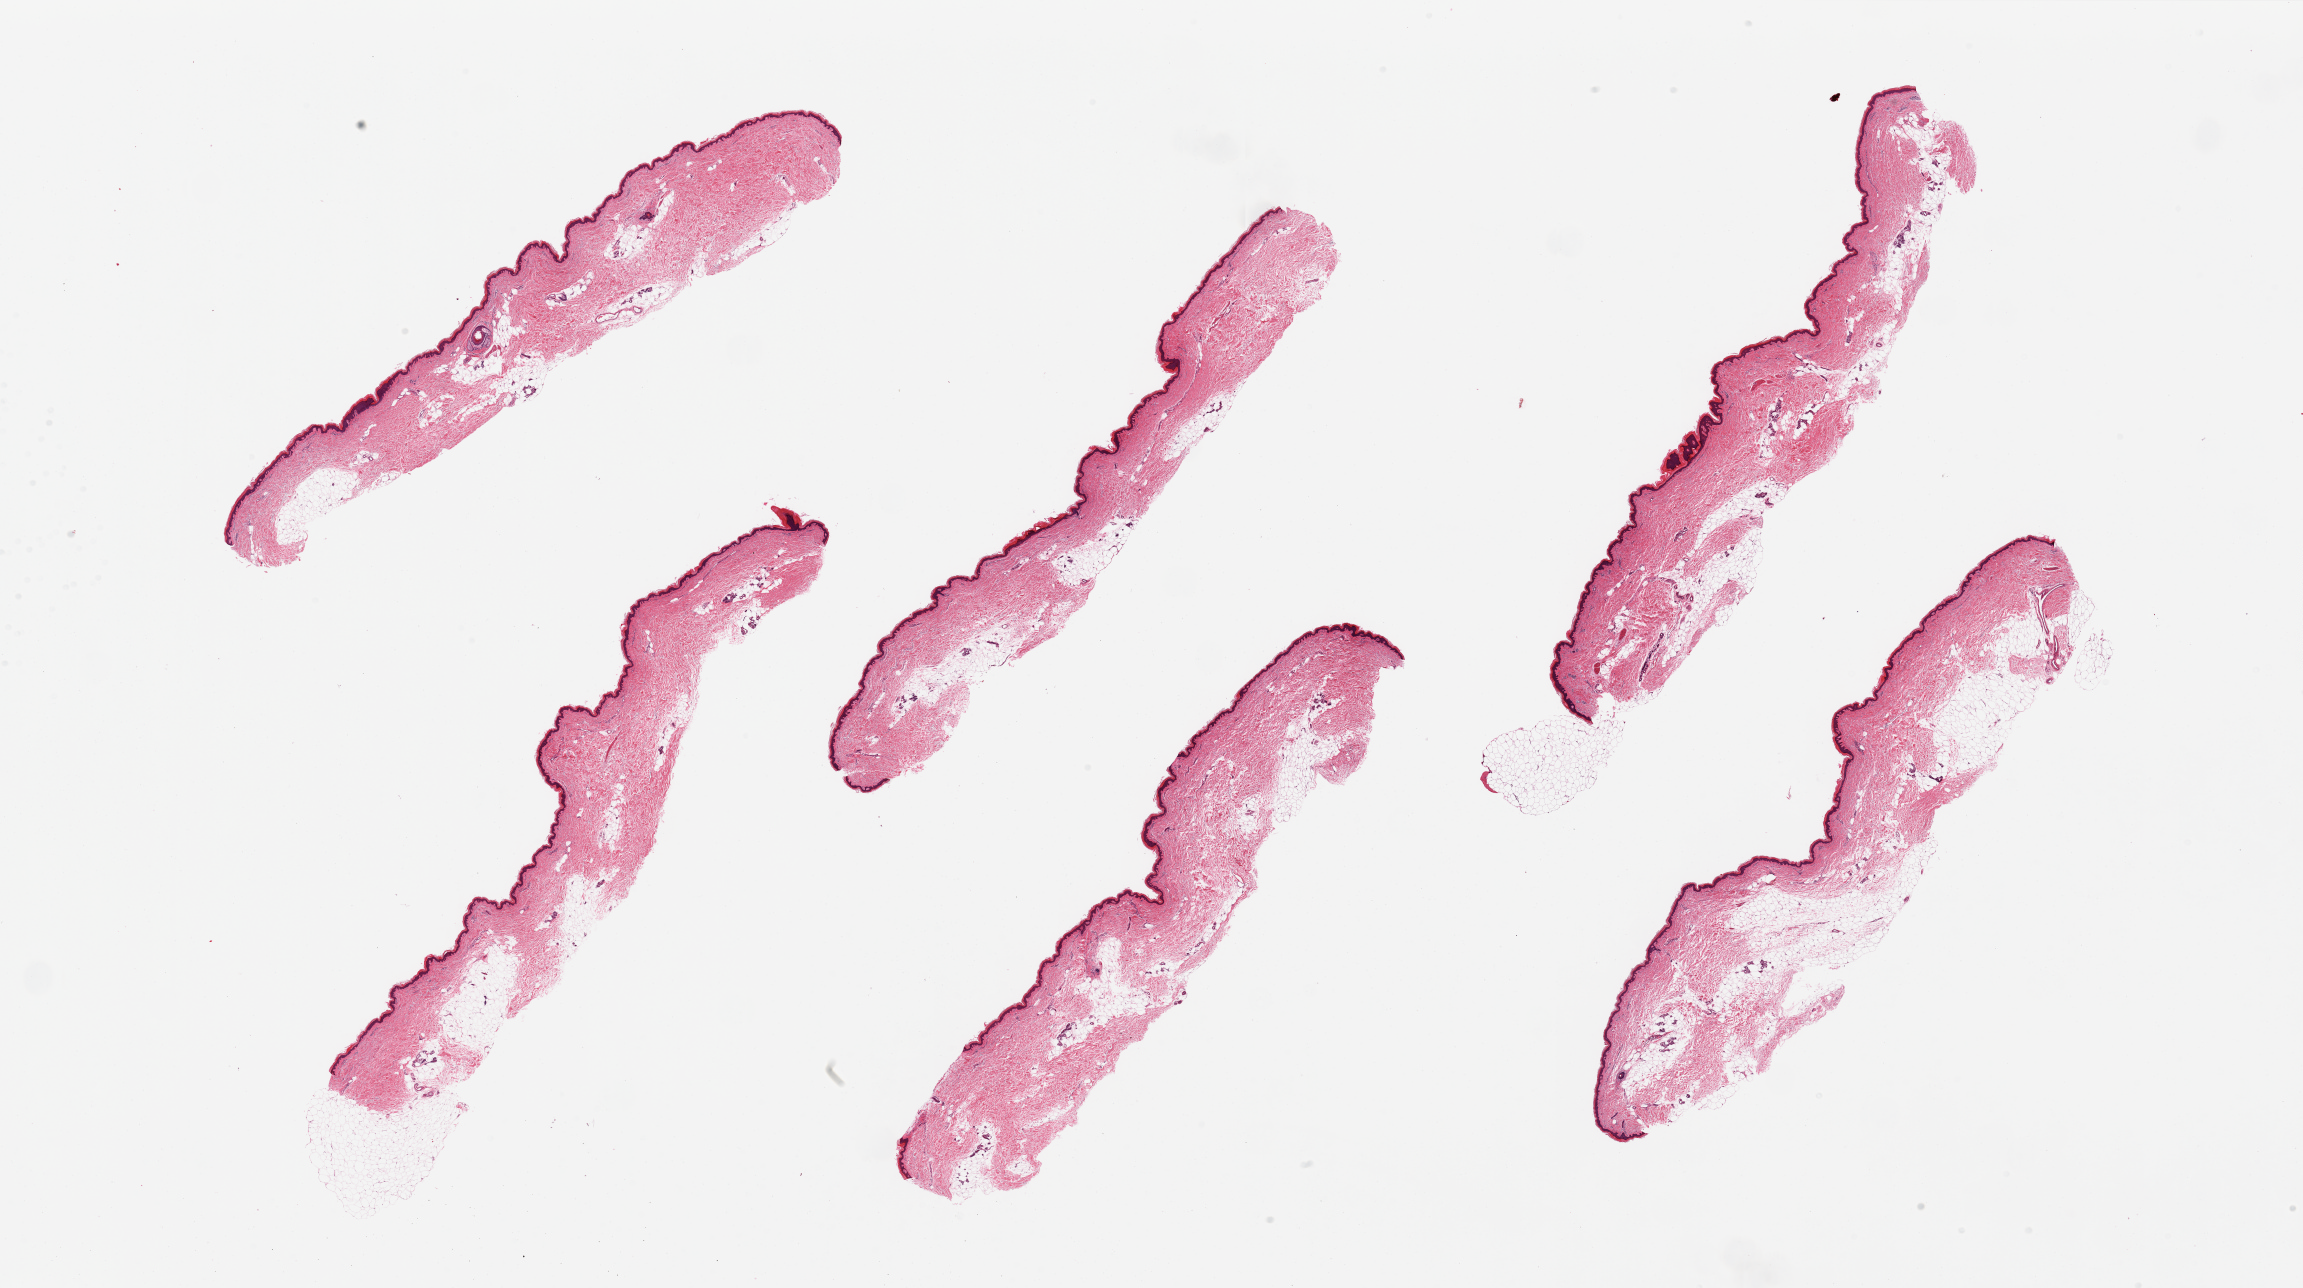
Digitized hematoxylin and eosin (H&E)-stained section, shown as a low-resolution overview of the whole scanned area (about 36.4 x 20.4 mm, slide scanned at 20x), PAXgene-fixed paraffin-embedded (PFPE) section, section of skin of lower leg (target tissue), donor tissue sample. Female donor.
Pathologist's review note for this sample: 6 pieces, includes 10-30% attached and internal fat, squamous epithelium measures 36 to 45 microns.